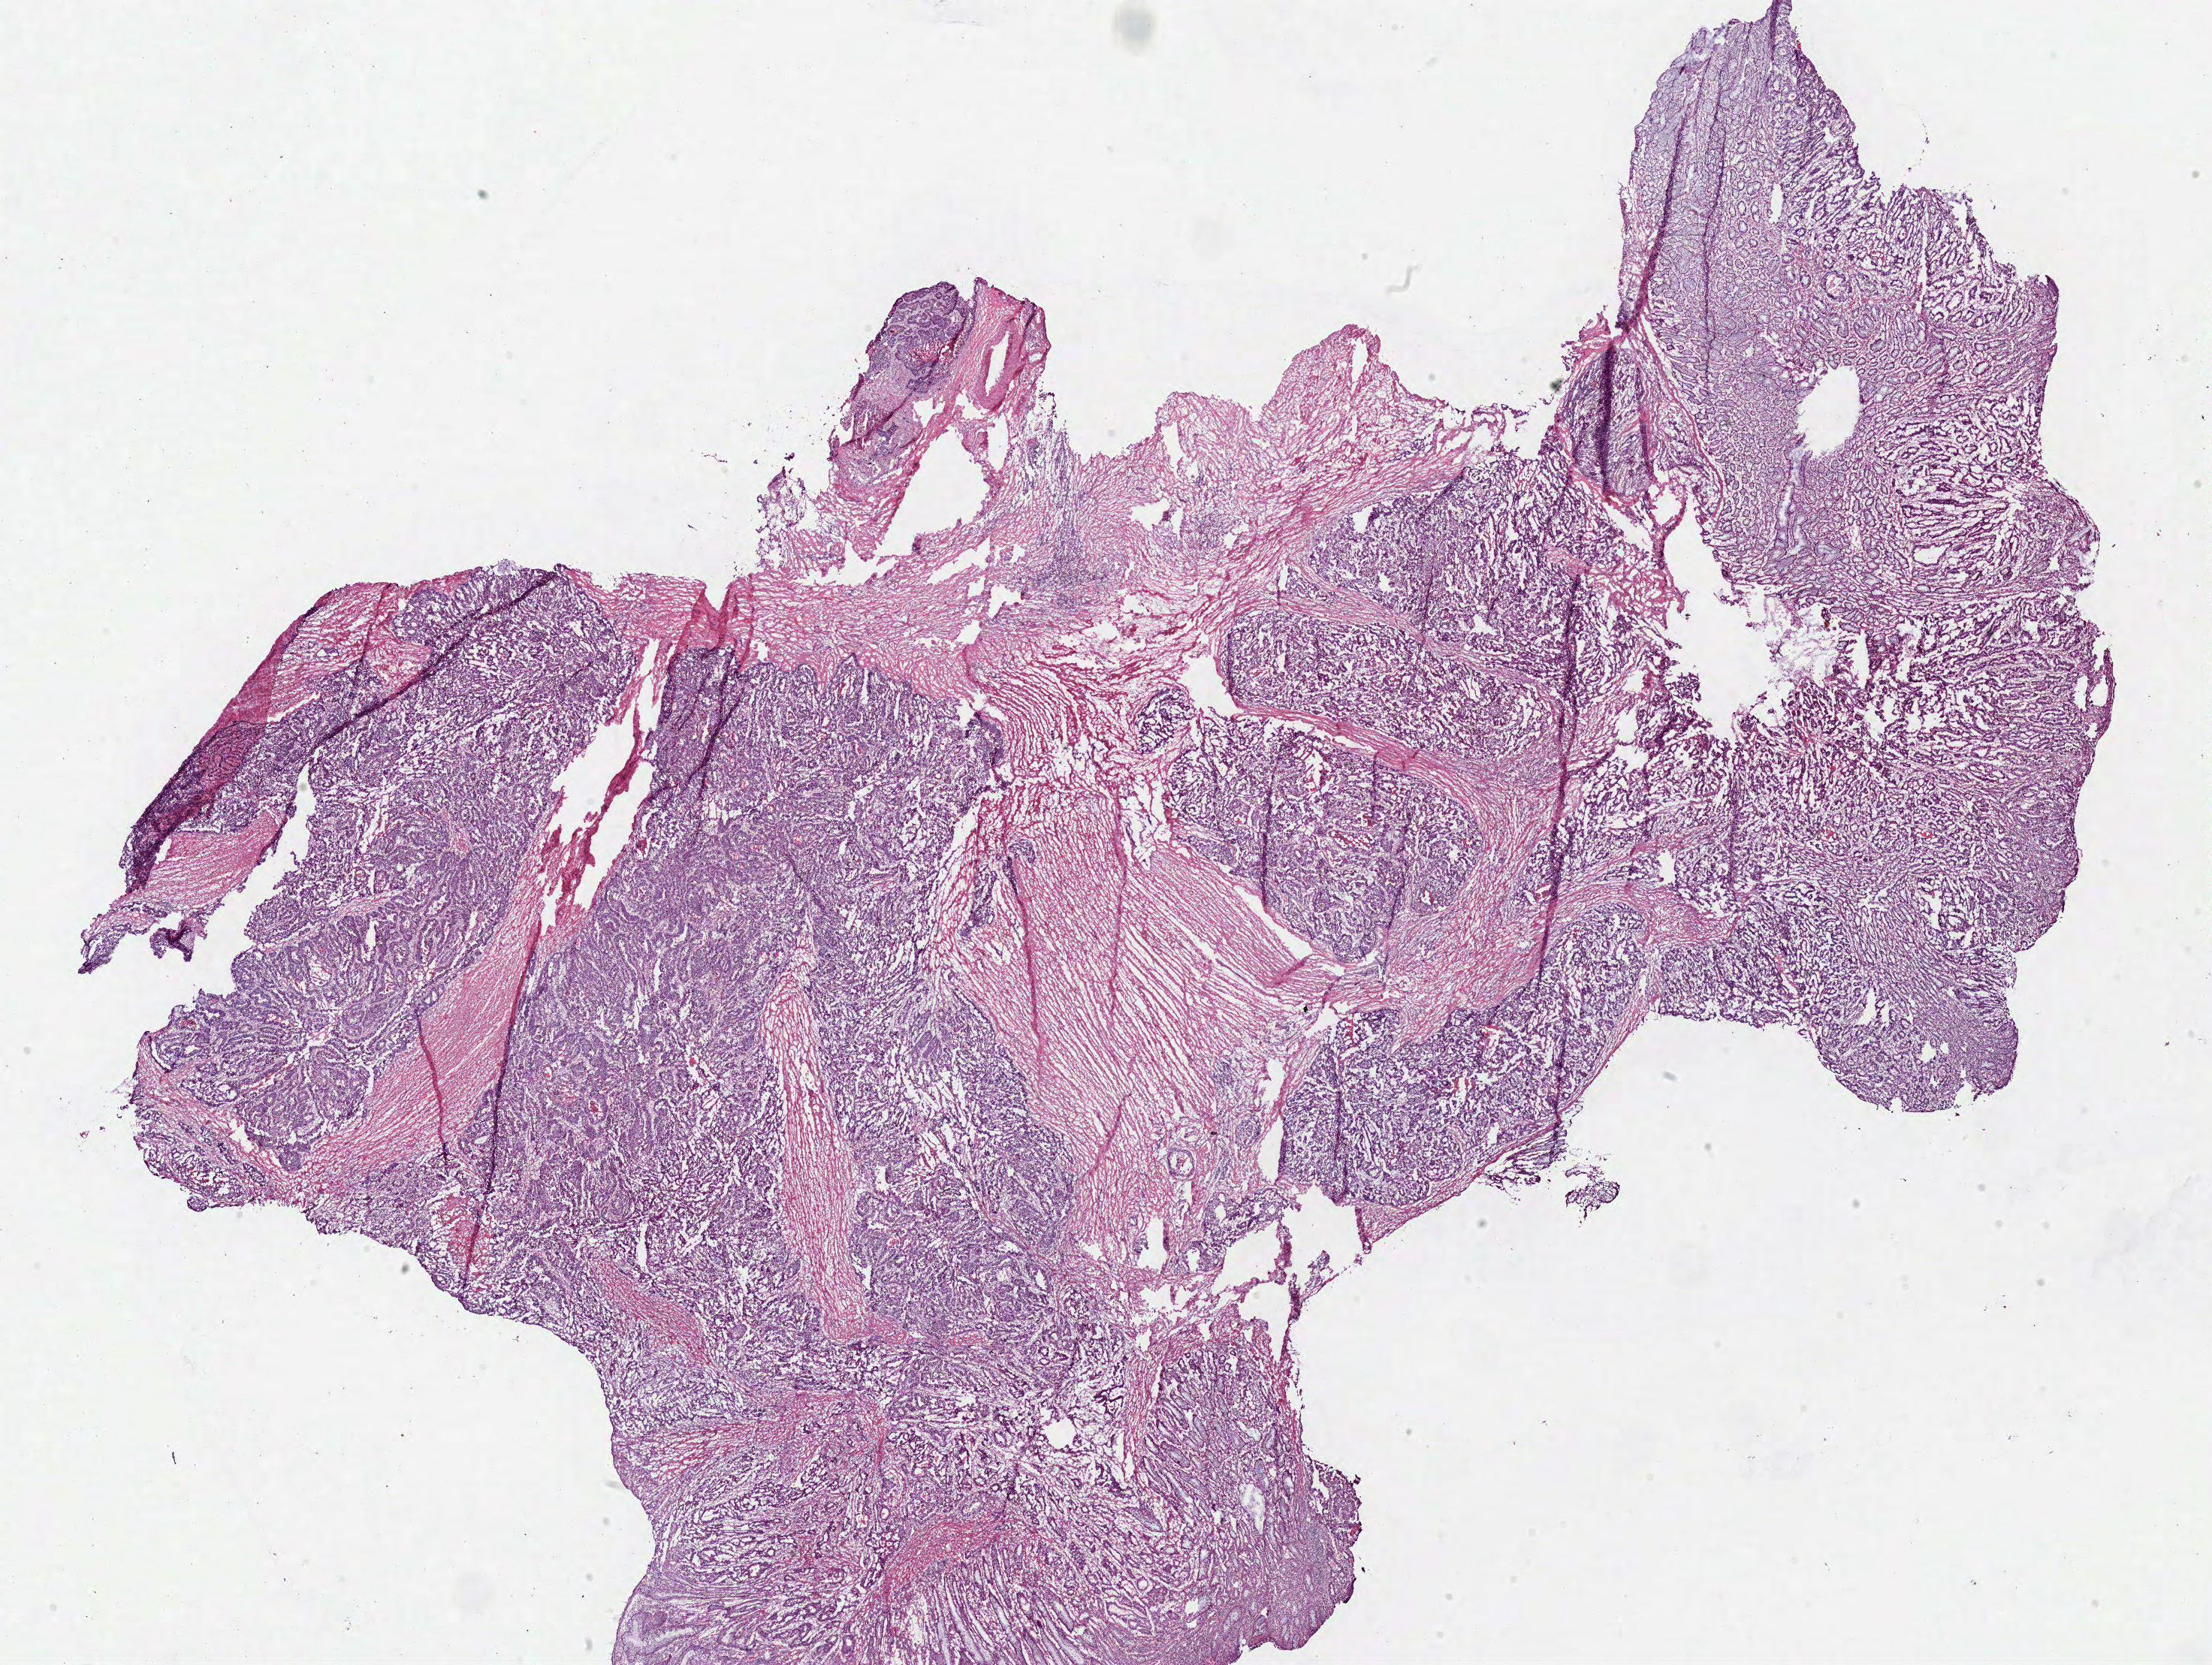
Digitized Hematoxylin and eosin (H&E) stained tissue section (whole slide), shown as a low-resolution overview of the whole scanned area (about 23.2 x 17.5 mm); frozen section from the bottom of the tissue portion; primary tumour sample from the colon. Female, age 51 years at initial diagnosis. Composition of this section per pathologist review: tumour cells 80%, tumour nuclei 75%, normal cells 10%, stromal cells 9%, necrosis 1%. Inflammatory infiltration, as recorded: lymphocyte infiltration 5%, monocyte infiltration 1%, neutrophil infiltration 1%.
• AJCC pathologic stage: IIIB (7th edition)
• diagnosis: Adenocarcinoma, NOS (sigmoid colon)
• lymph nodes positive (case pathology): 1 of 6 examined
• TNM: T3 N1 M0